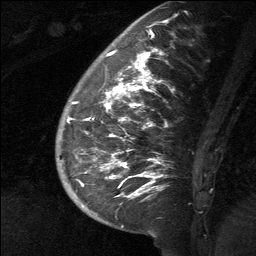
Breast MRI (dynamic contrast-enhanced), one sagittal slice. Position 21 of 64 along the scan axis. Dynamic contrast-enhanced study with each time point stored as its own series, time point 2 of 3 at this slice position (early post-contrast, ordered by acquisition time). 1.5 T. TE 4.8 ms, TR 27 ms. 2 mm slice thickness. 256 × 256 image matrix, field of view 180 × 180 mm. Female patient, age 39 years. Case-level facts recorded for this patient, not image findings: setting: breast cancer imaged before/during neoadjuvant chemotherapy; receptor status: HER2-positive.
Outlined on this slice (semi-automatically segmented with operator editing):
- analysis volume of interest (the breast-tissue region the enhancement analysis was run in; not a lesion): box from (x=58, y=40) to (x=201, y=217) px
- tumour enhancement mask (voxels above the 90 % enhancement threshold inside the analysis volume of interest): (x=68, y=50)–(x=163, y=199)